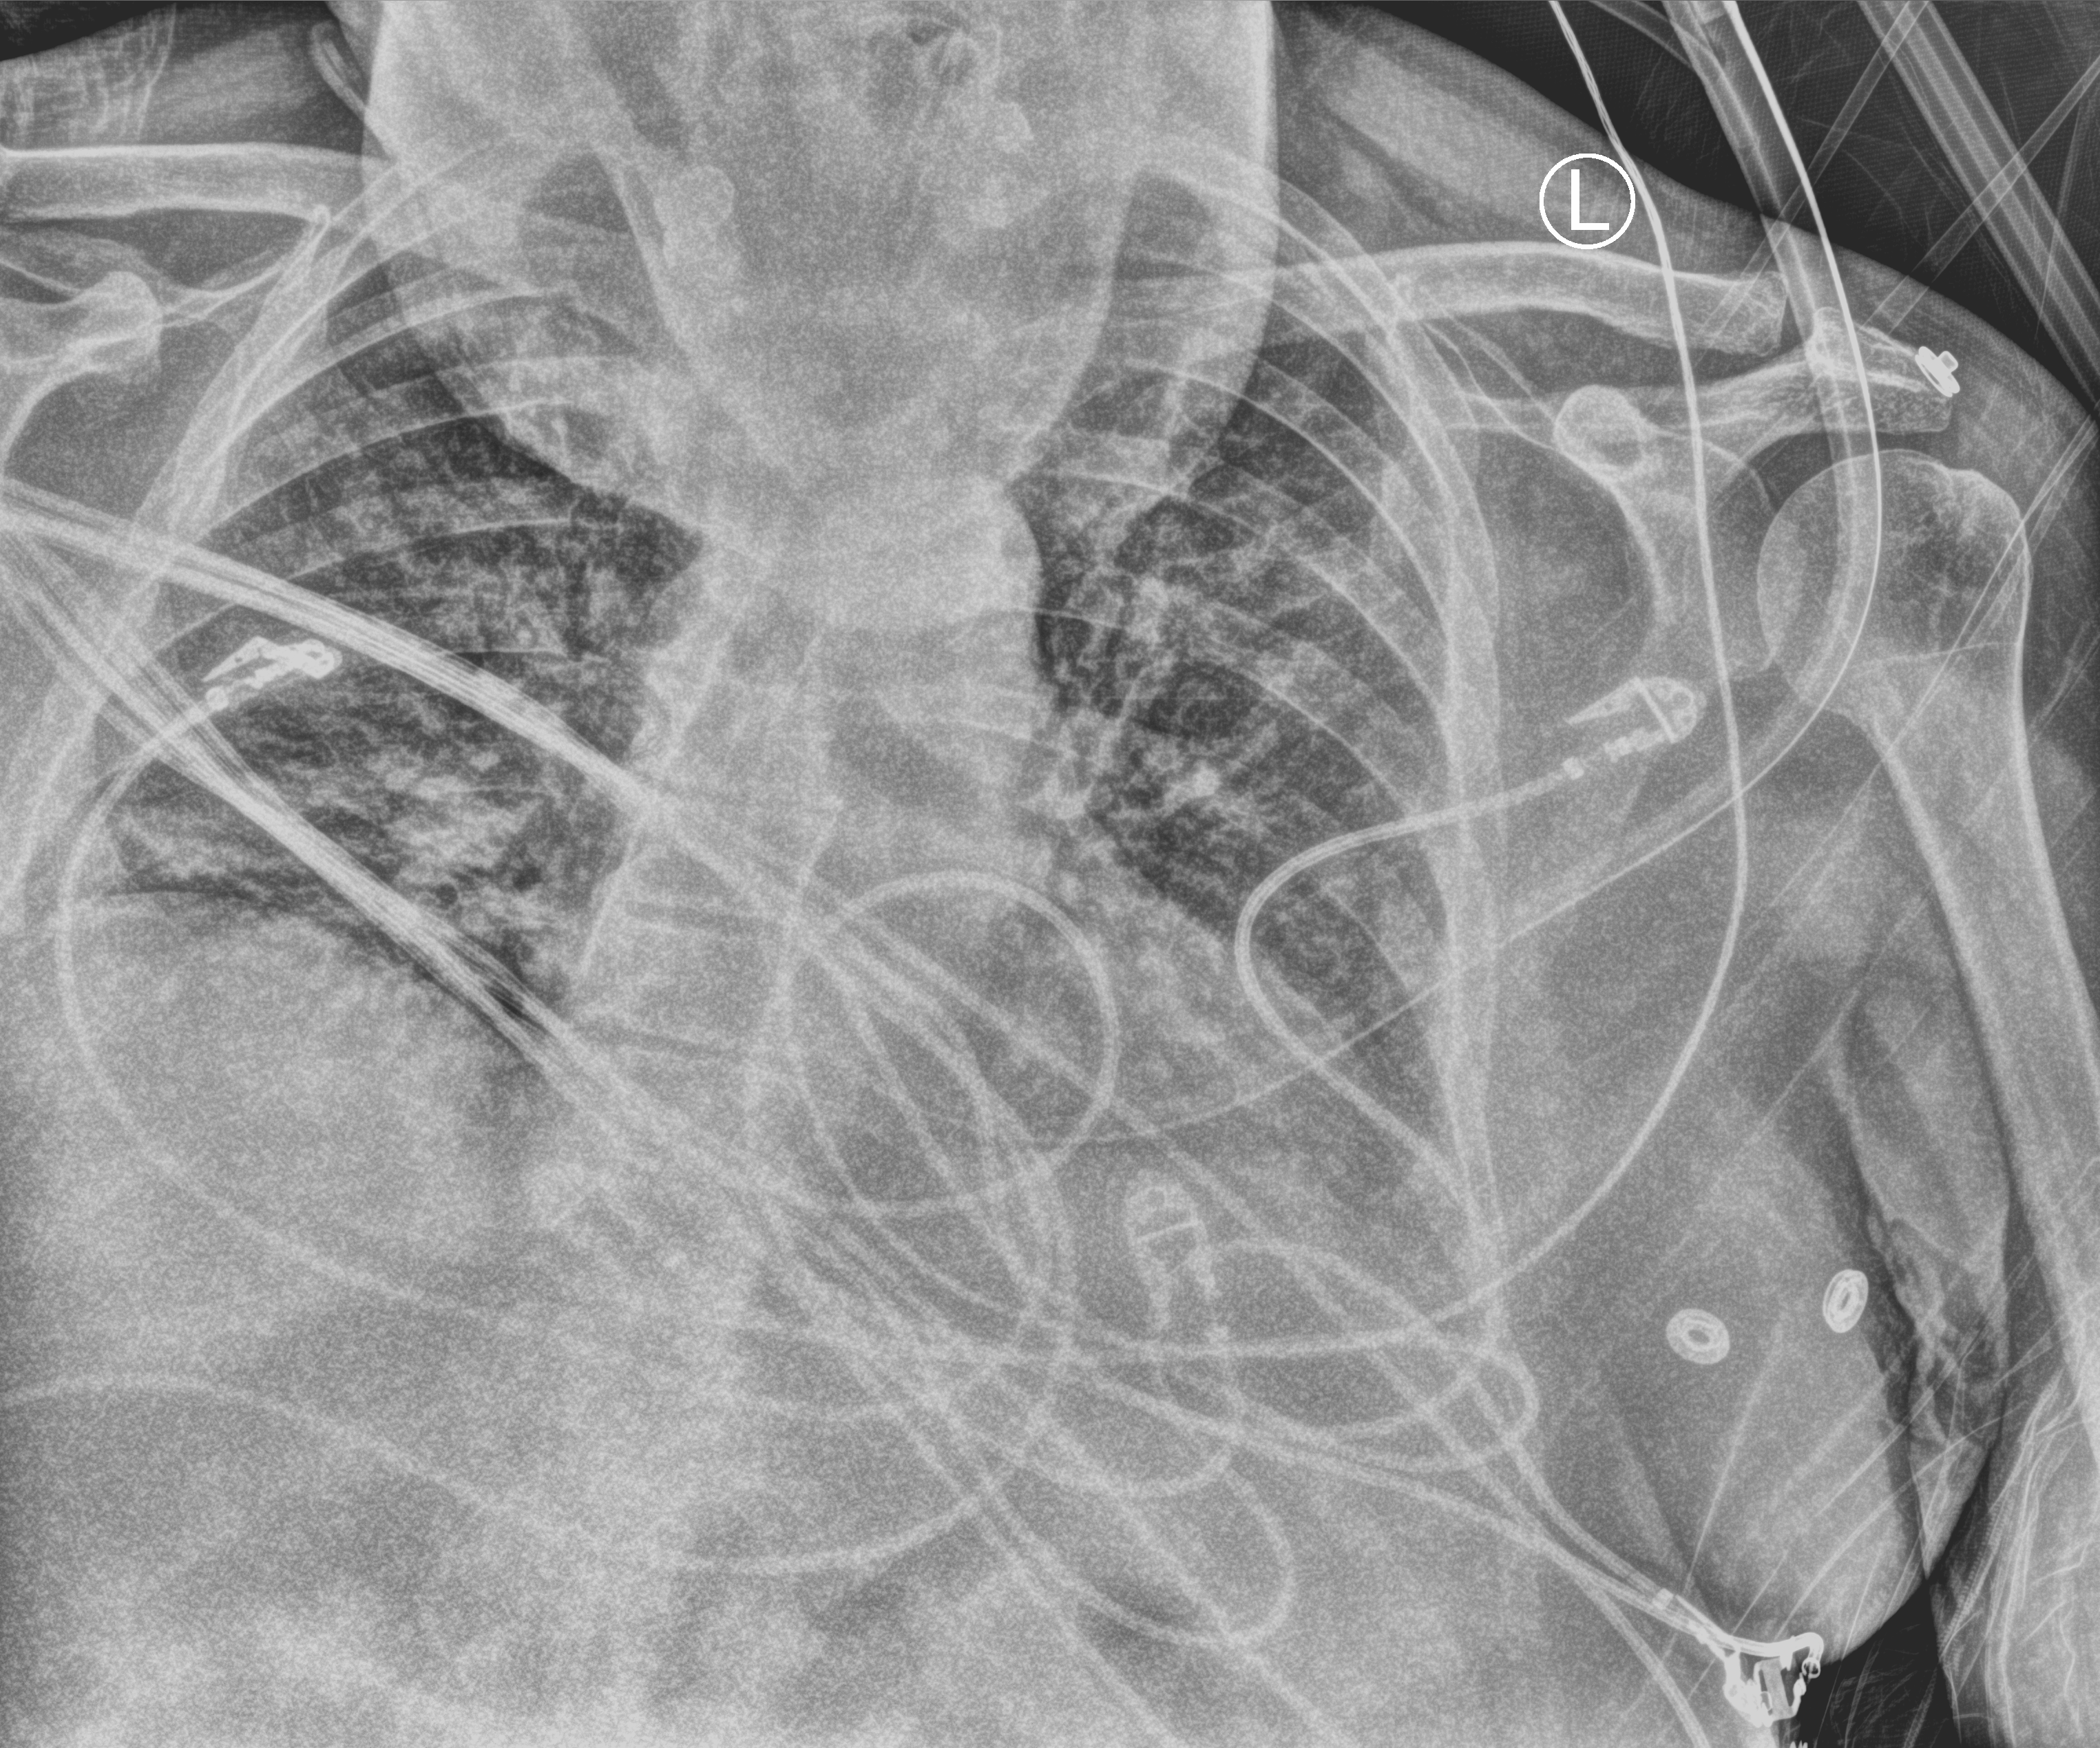
Bedside chest radiograph (computed radiography); anteroposterior (AP) projection. Patient hospitalised with COVID-19; male, aged 60–74 years.
From the hospital-stay record, not from the radiograph (when in the stay this image was taken is not recorded): diabetes (admission record): no.